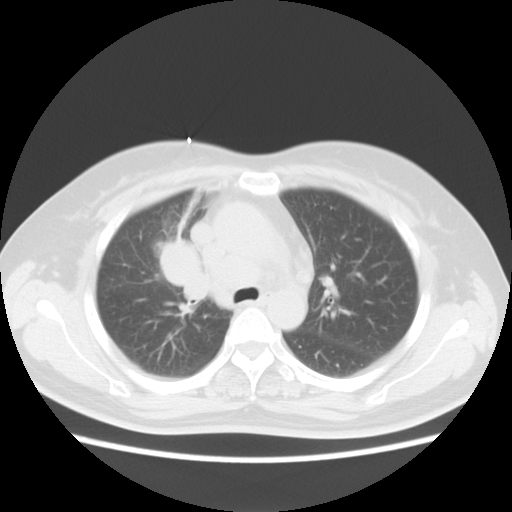
Chest CT, one axial slice; slice 9 of 18 in the series (ordered by position); 120 kVp; lung window (W 1500 / L -600 HU); 5 mm slice thickness; 512 × 512 image matrix. Female patient, age 54 years. Case-level facts recorded for this patient, not image findings: clinical TNM (as recorded): T2 N3 M0.
Structures marked on this image (bounding box drawn by a radiologist):
- lung tumour (recorded histology: small cell carcinoma): box from (x=153, y=238) to (x=211, y=303) px